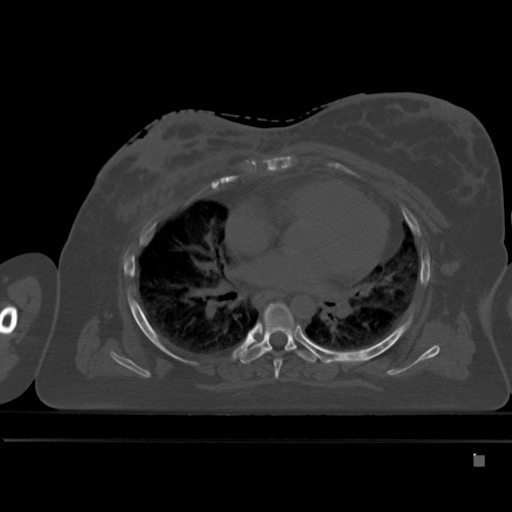
CT including the spine, one axial slice; slice 311 of 495 in the series (ordered by position); bone window (W 1800 / L 400 HU); 1.5 mm slice thickness; 512 × 512 image matrix, field of view 404 × 404 mm. Patient: female, 33 years. Case-level facts recorded for this patient, not image findings: primary cancer: breast; vertebrae with lytic lesions (as recorded): T1.
Annotated regions visible in this slice (semi-automatically segmented with operator editing):
- T5 vertebra: bounding box (x1, y1, x2, y2) in pixels: (274, 360, 282, 379)
- T6 vertebra: (240, 303, 320, 364)